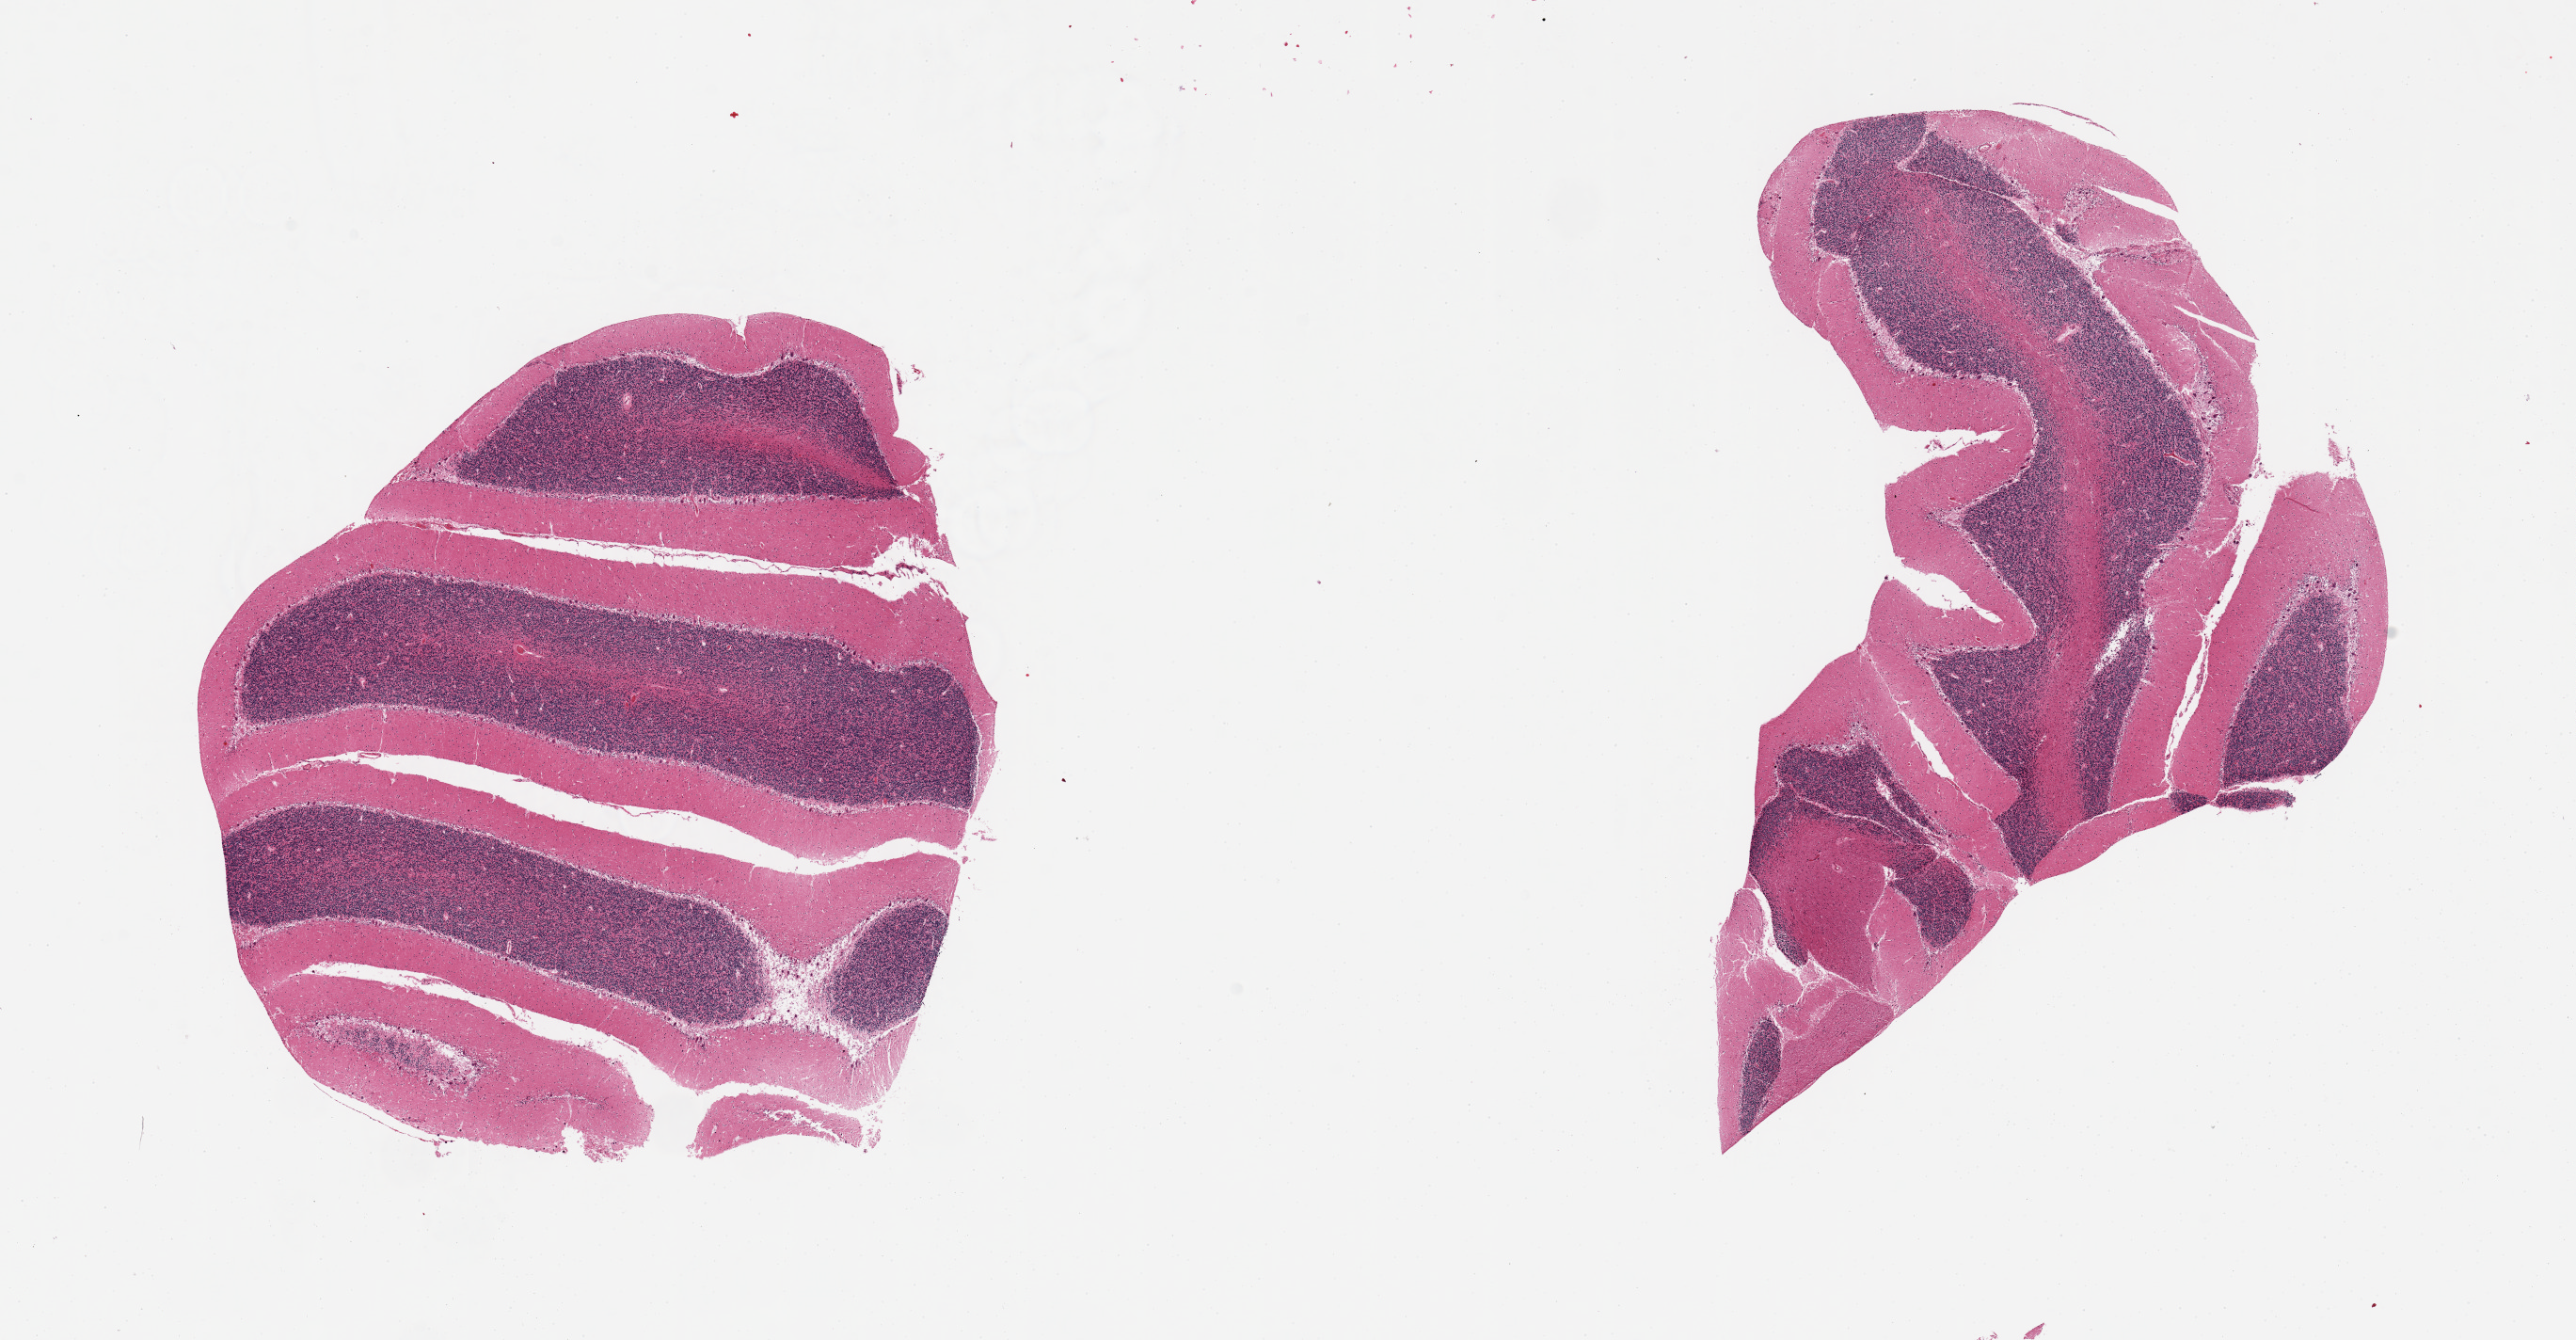
Whole-slide image, hematoxylin and eosin (H&E) stain, brightfield — whole scanned area (about 21.7 x 11.3 mm) shown as a low-resolution overview, PAXgene-fixed, paraffin-embedded tissue, target tissue: cerebellum, tissue donor sample. Donor: male.
Reviewer comment on this tissue sample: 2 pieces.